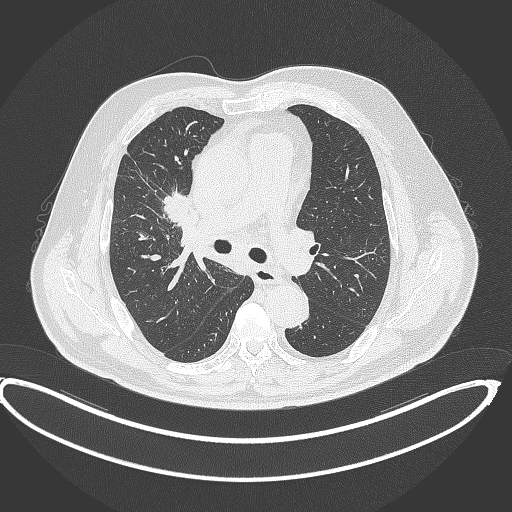
Chest CT, one axial slice; slice 253 of 390 in the series (ordered by position); reconstruction kernel B70f; lung window (W 1500 / L -600 HU); 1 mm slice thickness; 512 × 512 image matrix. Patient: male, 62 years. Case-level facts recorded for this patient, not image findings: clinical TNM (as recorded): T1c N3 M1c.
Annotated regions visible in this slice (bounding box drawn by a radiologist):
- lung tumour (recorded histology: adenocarcinoma): bounding box <161,191,191,223> (left, top, right, bottom; pixels)